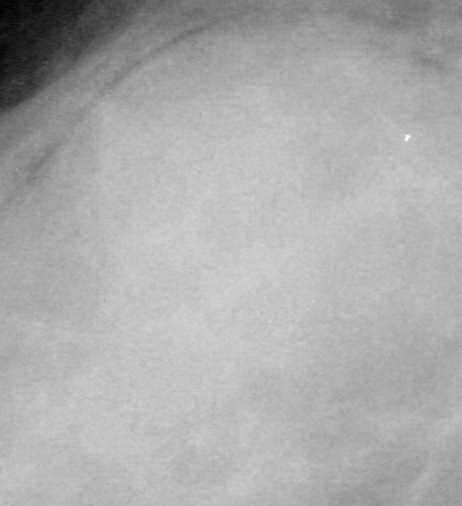
Cropped region of a digitized screen-film mammogram centred on a radiologist-marked abnormality, left breast, CC view.
- Finding: mass, shape oval, margins obscured; BI-RADS assessment category 4; subtlety rating 4 on a 1 (subtle) to 5 (obvious) scale; pathology (as recorded): benign.